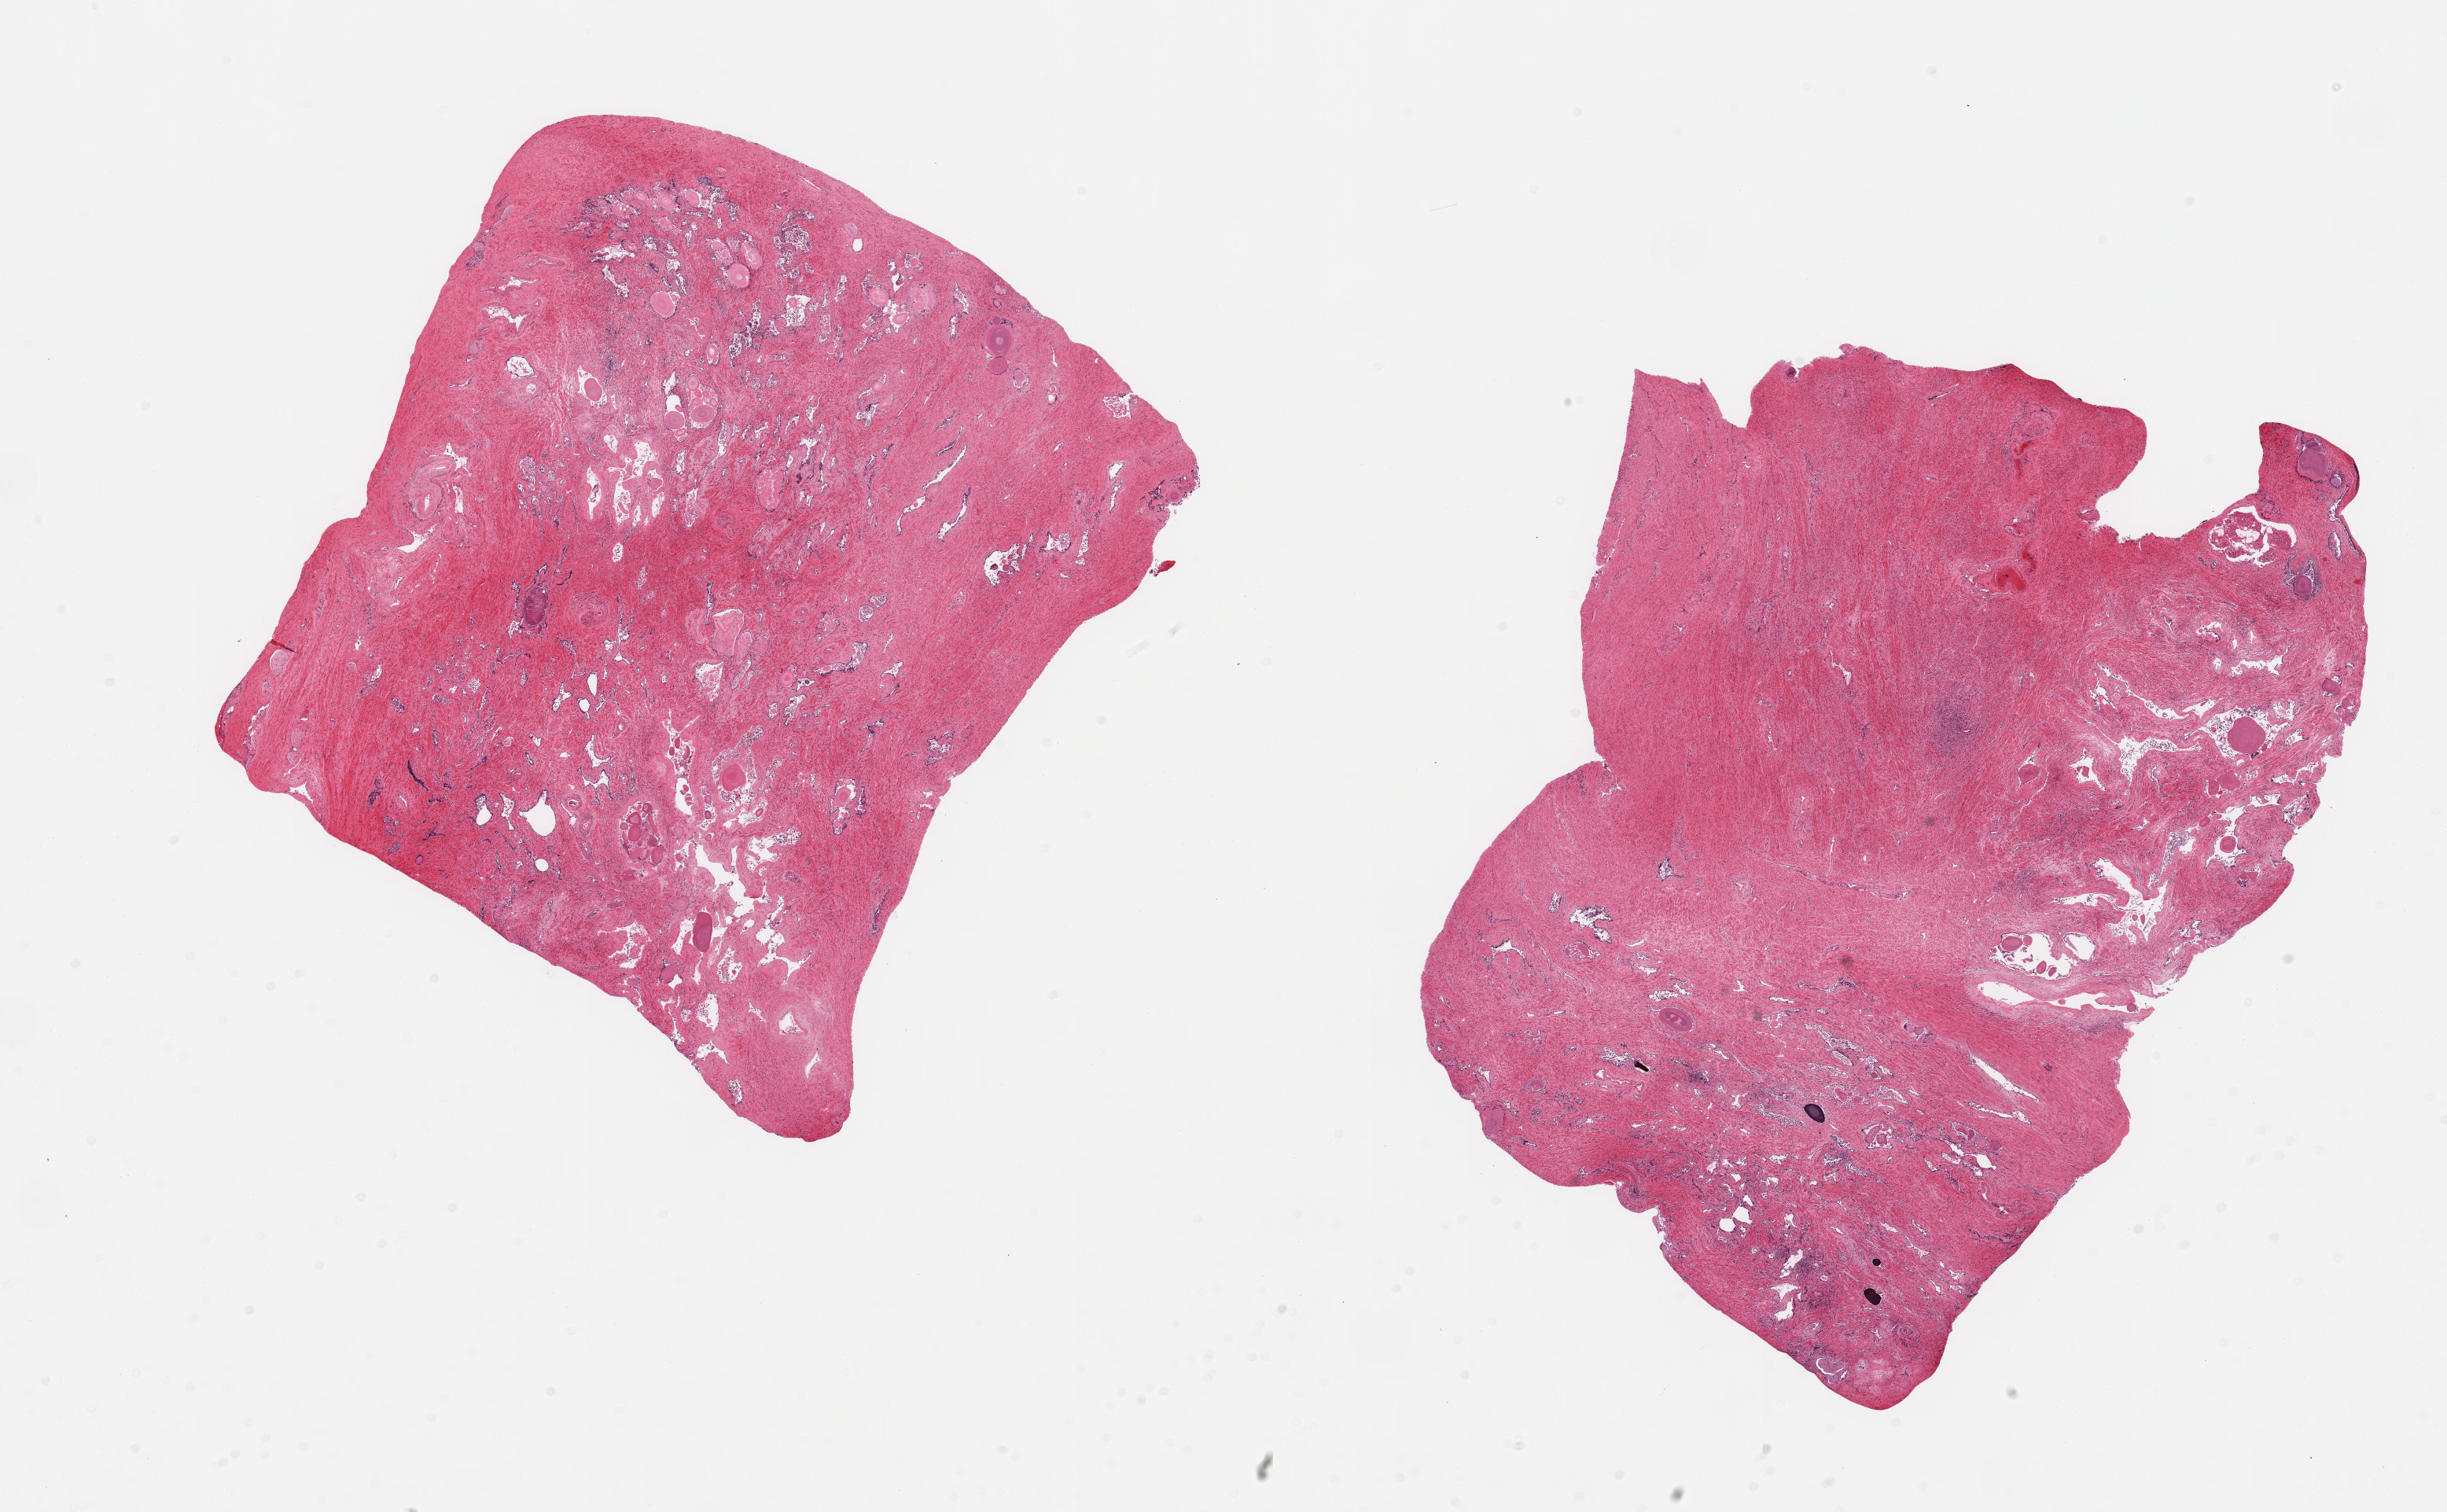
Whole-slide image, hematoxylin and eosin (H&E) stain, whole scanned area (about 24.6 x 15.2 mm) shown as a low-resolution overview, PAXgene-fixed paraffin-embedded (PFPE) section, section of prostate (target tissue), tissue donor sample. Male donor.
Pathologist's review note for this sample: 2 pieces; glandular epithelium severely autolyzed; stroma intact.